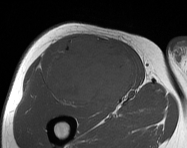
MRI of an extremity soft-tissue mass, one axial slice; position 92 of 114 along the scan axis; MR volume resampled by the dataset authors to the PET/CT grid (not the native acquisition matrix); 187 × 148 image matrix, field of view 183 × 145 mm. Male patient. From the clinical record (not read from this slice): histological type: pleiomorphic leiomyosarcoma; grade: intermediate; site of the primary tumour: right thigh.
Structures marked on this image (expert contour drawn on MRI and transferred to this co-registered scan by the dataset authors):
- gross tumour volume including surrounding oedema: bounding box <45,34,135,108> (left, top, right, bottom; pixels)
- gross tumour volume (mass): <47,34,135,108>